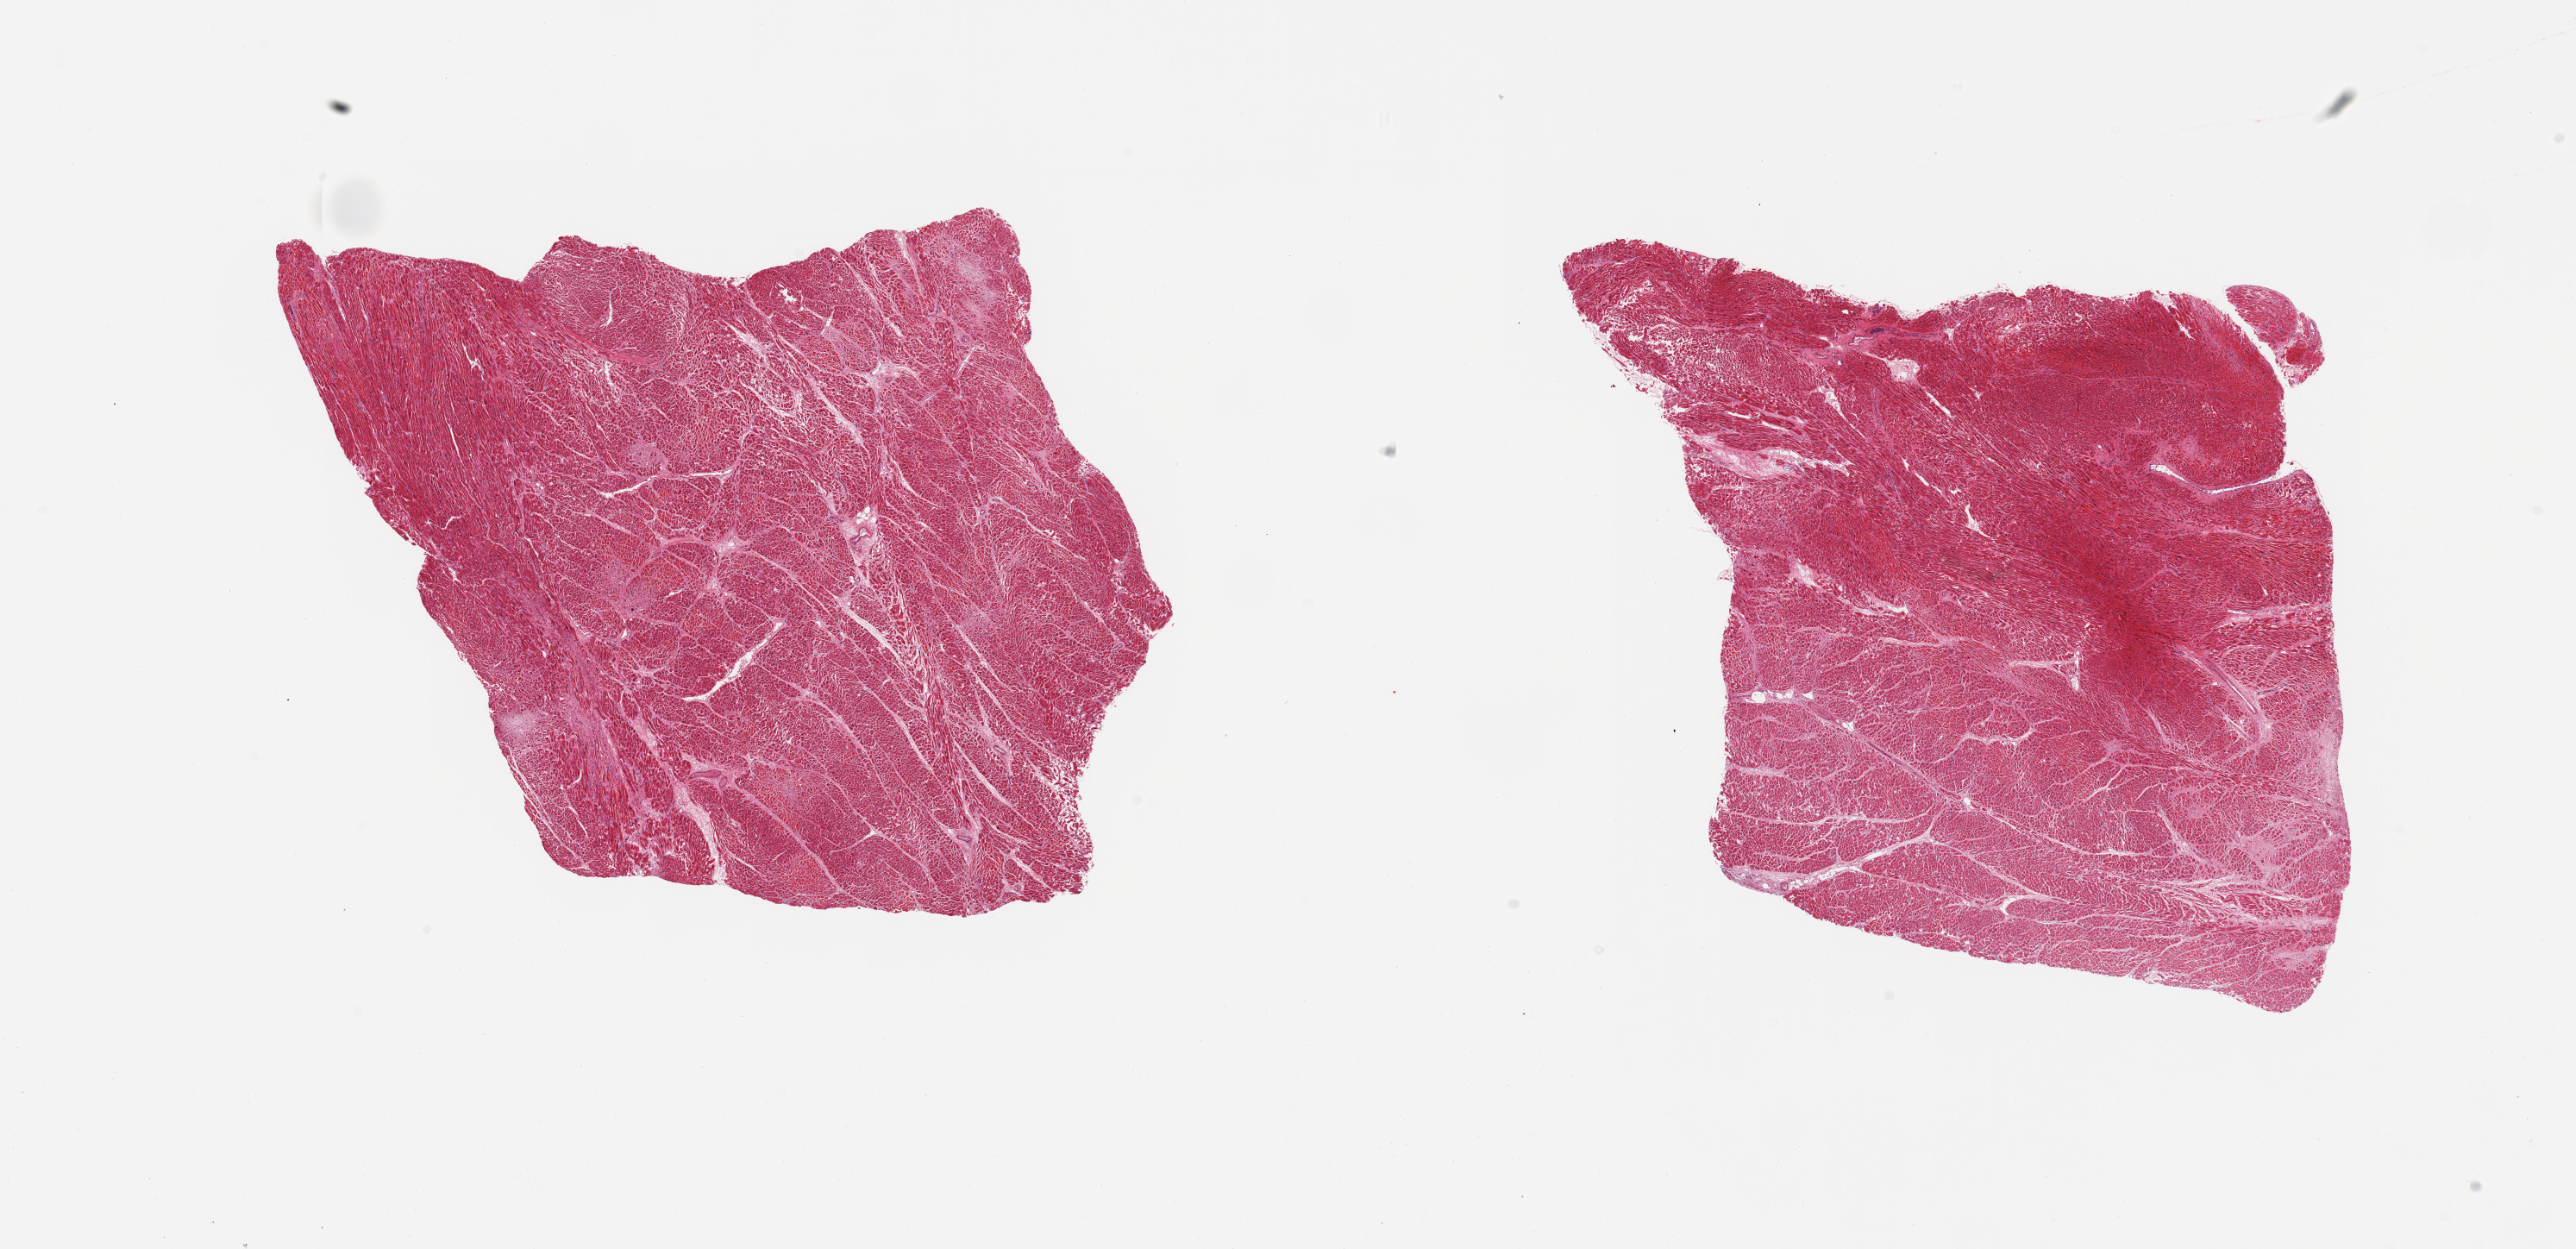
Haematoxylin and eosin whole-slide image, low-resolution overview of the scanned area, about 23.6 x 11.5 mm. PAXgene-fixed, paraffin-embedded tissue. Sampled site (target tissue): heart. Tissue donor sample. Donor sex: female.
* review note (as recorded): 2 pieces; patchy eosinophilia consistent with early ischemic change, hypertrophy, patchy fibrosis